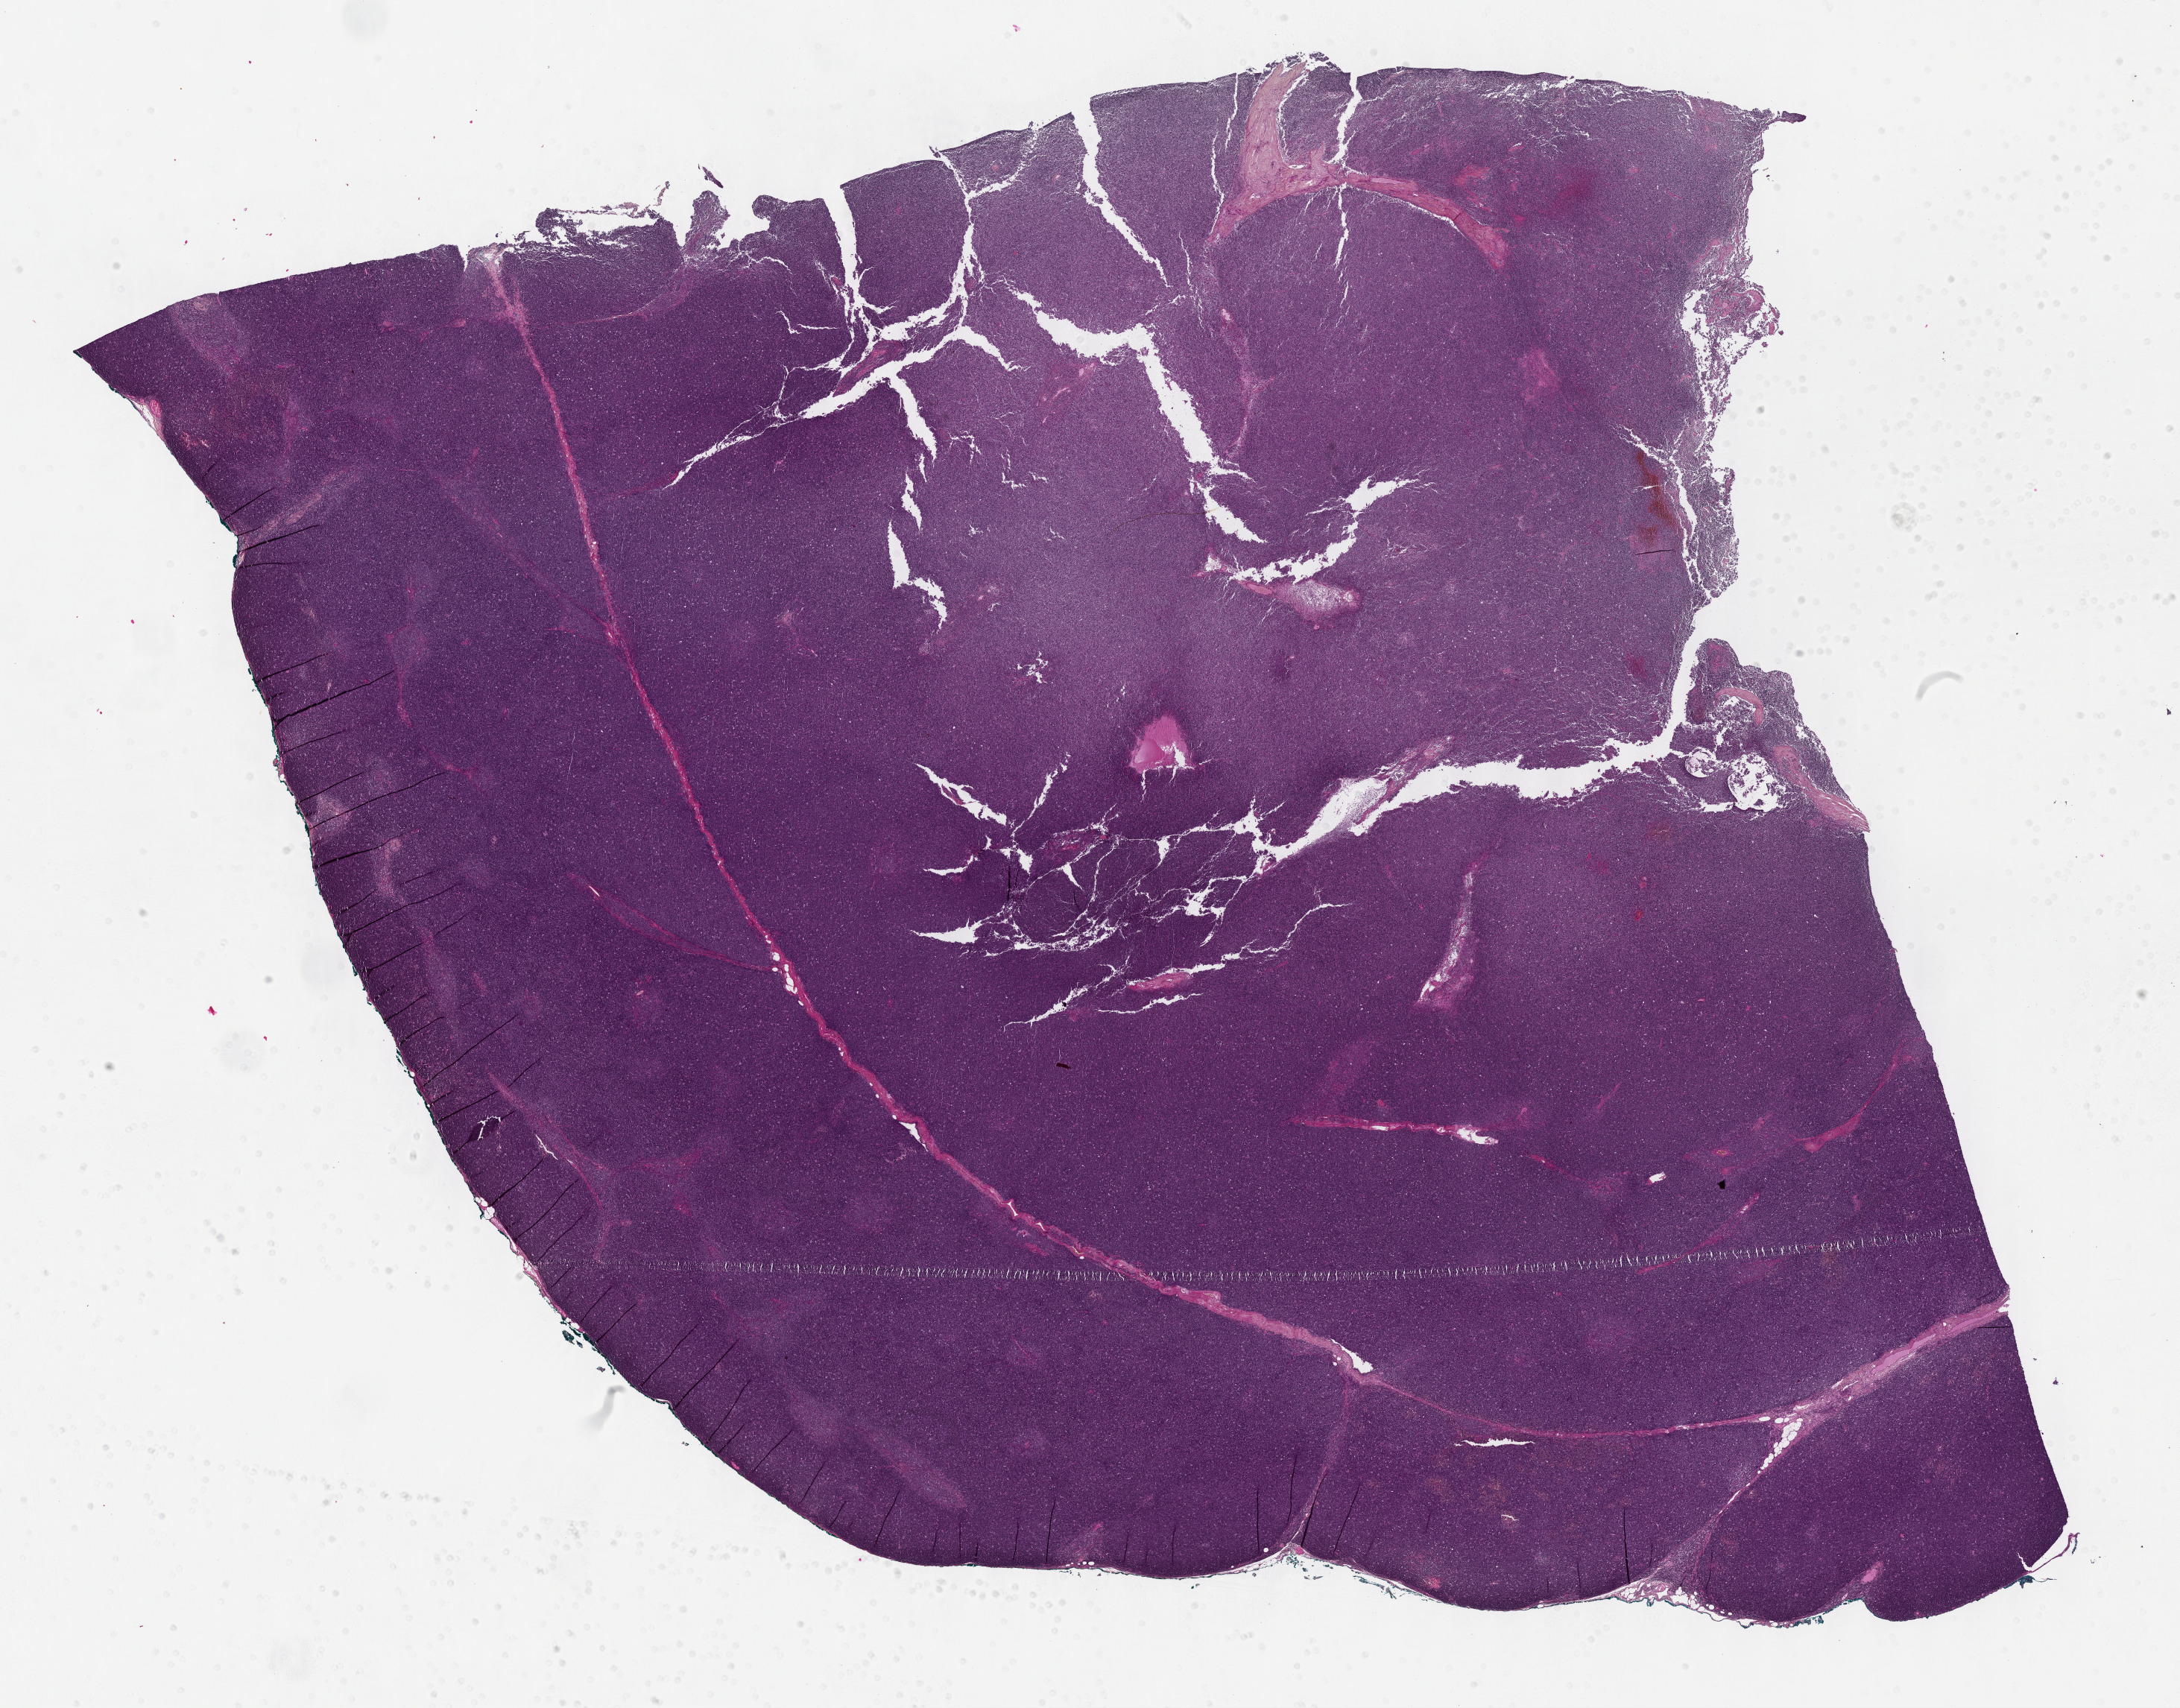
Hematoxylin and eosin (H&E) stained whole-slide image, low-resolution overview of the scanned area, about 23.7 x 18.5 mm (acquisition: 40x scan), formalin-fixed paraffin-embedded (FFPE) diagnostic section, sample: primary tumour, thymus. Female patient; age at initial diagnosis 79 years.
Histologic diagnosis: Thymoma, type B1, malignant.